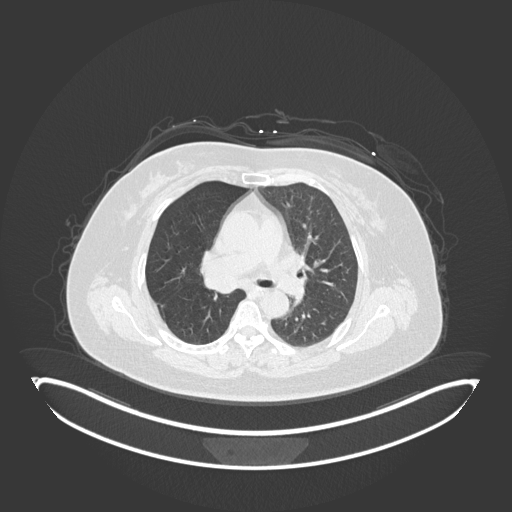
Chest CT, one axial slice; slice 100 of 245 in the series (ordered by position); reconstruction kernel B30f; 120 kVp; lung window (W 1500 / L -600 HU); 1 mm slice thickness; 512 × 512 image matrix, field of view 500 × 500 mm. Female patient, age 60 years. From the clinical record (not read from this slice): clinical TNM (as recorded): T1c N0 M0; histopathological grade: G1-G2.
Annotated regions visible in this slice (bounding box drawn by a radiologist):
- lung tumour (recorded histology: squamous cell carcinoma): box from (x=201, y=264) to (x=244, y=295) px